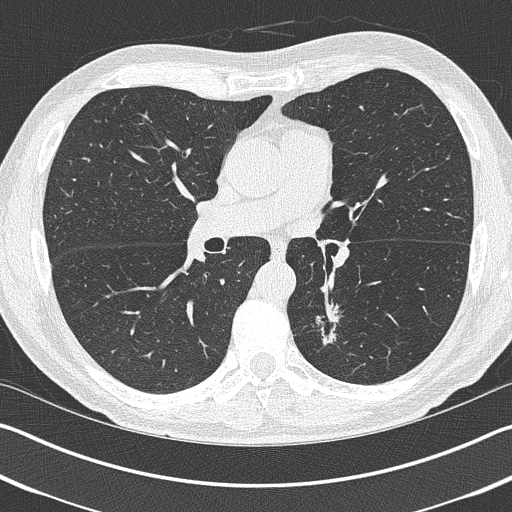
Low-dose screening chest CT, one axial slice; slice 229 of 402 in the series (ordered by position); reconstruction kernel B50f; lung window (W 1500 / L -600 HU); 512 × 512 image matrix.
Structures marked on this image (manually delineated by an expert):
- lesion 1 (tumor, lower lobe of left lung): bounding box <316,302,340,345> (left, top, right, bottom; pixels)